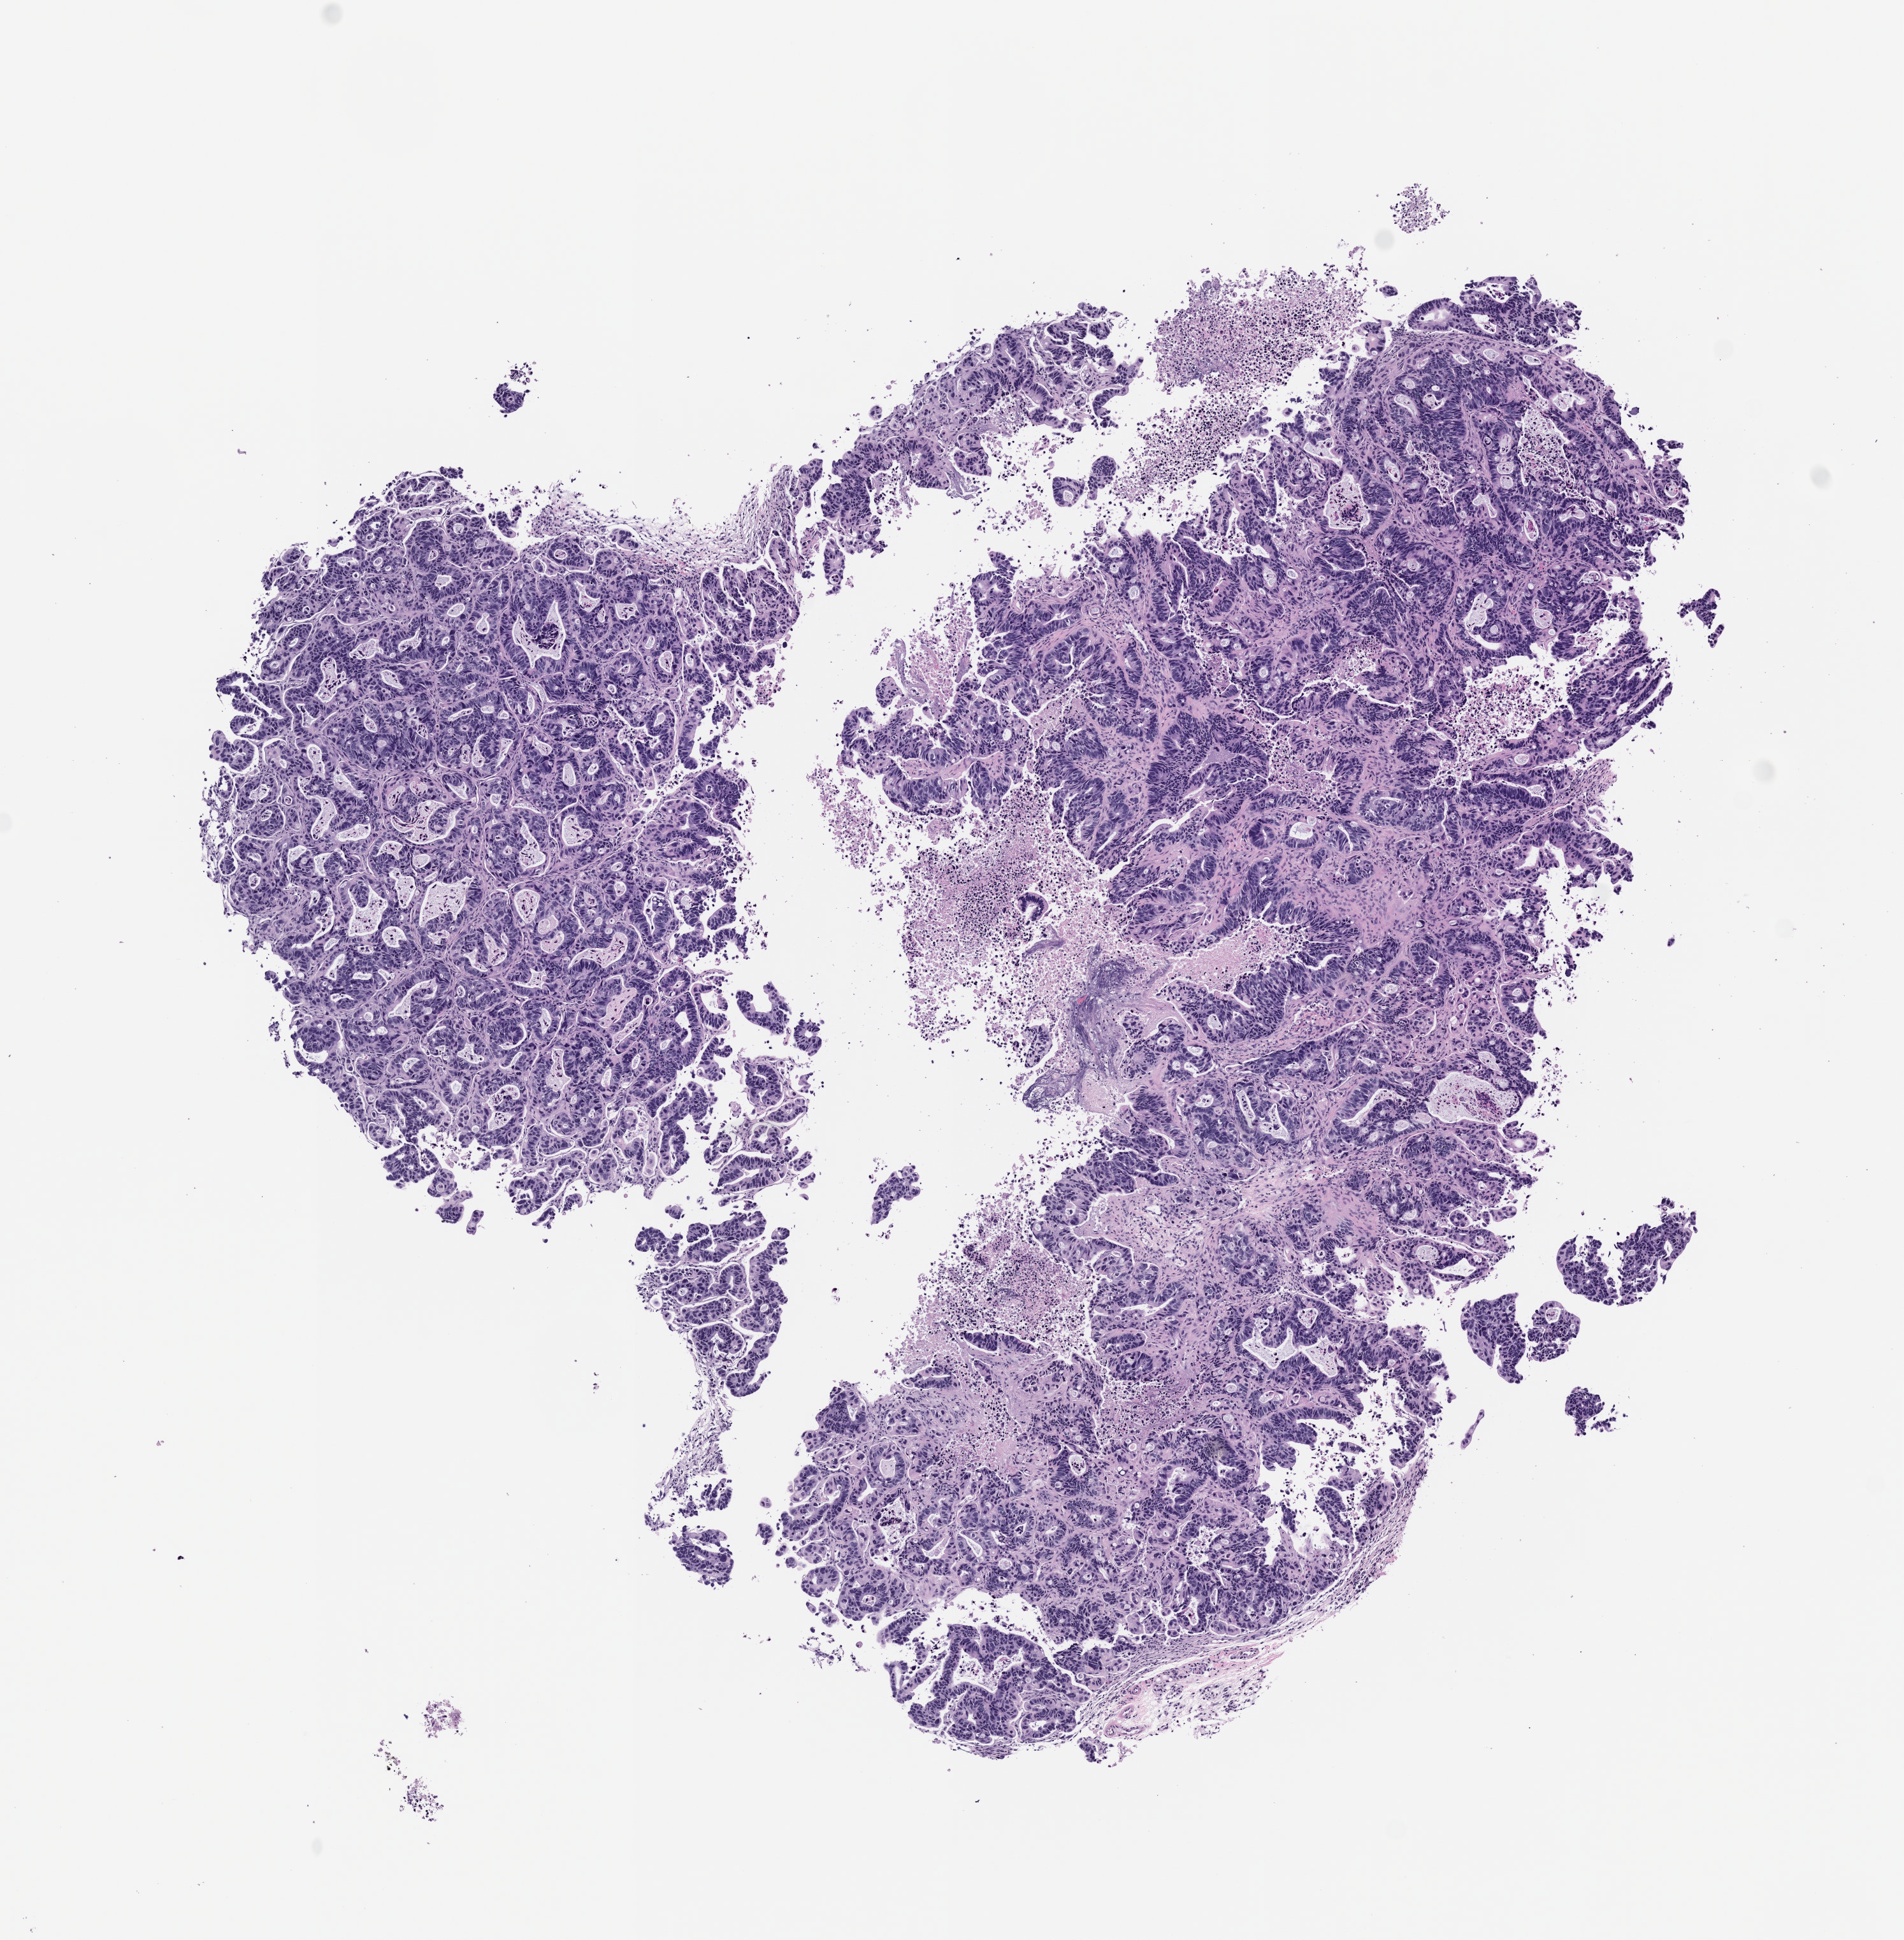
Whole-slide image, haematoxylin and eosin: patient-derived xenograft (human tumor grown in a mouse), passage 3, whole scanned area (about 6.0 x 6.1 mm) shown as a low-resolution overview, formalin-fixed paraffin-embedded section, tumor site category: colon.
• originating patient diagnosis: Colon Adenocarcinoma